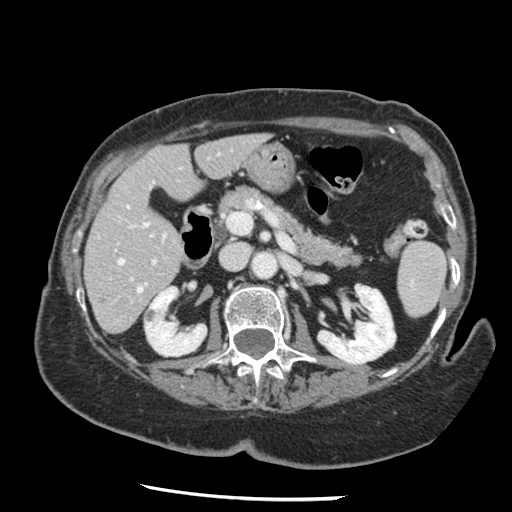
Contrast-enhanced abdominal CT, one axial slice; position 64 of 148 along the scan axis; 120 kVp; soft-tissue window (W 400 / L 40 HU); 512 × 512 image matrix, field of view 330 × 330 mm. Female patient, age 85 years. From the clinical record (not read from this slice): diagnosis: colorectal cancer liver metastases, imaged before liver resection; multiple liver metastases: no; largest metastasis: 0.9 cm; disease in both lobes: no.
Structures marked on this image (outlined manually by an expert reader):
- hepatic veins: bounding box [x1, y1, x2, y2] px = [118, 259, 146, 292]
- liver: [85, 135, 265, 333]
- planned liver remnant (the part of the liver to remain after resection): [85, 135, 265, 323]
- portal vein (with intrahepatic branches): [127, 205, 157, 281]
- liver metastasis: [100, 297, 106, 303]